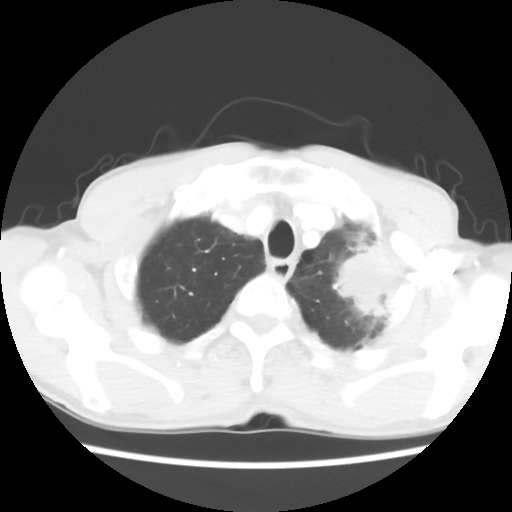
Chest CT, one axial slice. Slice 52 of 60 in the series (ordered by position). Reconstruction kernel STANDARD. Lung window (W 1500 / L -600 HU). 5 mm slice thickness. 512 × 512 image matrix, field of view 308 × 308 mm. Male patient, age 64 years. From the clinical record (not read from this slice): clinical TNM (as recorded): T3 N3 M0.
Outlined on this slice (bounding box drawn by a radiologist):
- lung tumour (recorded histology: adenocarcinoma): bounding box (x1, y1, x2, y2) in pixels: (328, 239, 402, 327)